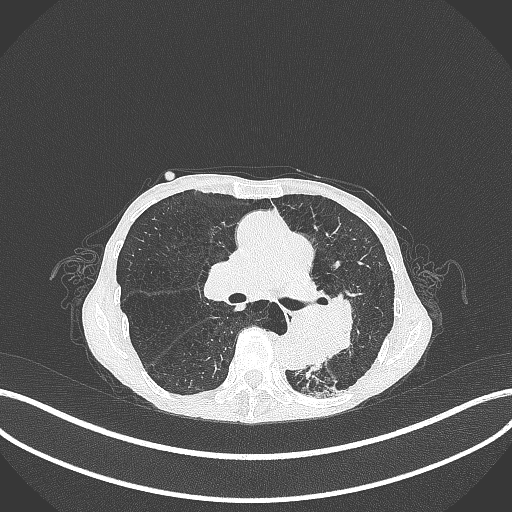
Chest CT, one axial slice; position 160 of 347 along the scan axis; 120 kVp; lung window (W 1500 / L -600 HU); 512 × 512 image matrix, field of view 400 × 400 mm. Patient: female, 70 years. Case-level facts recorded for this patient, not image findings: clinical TNM (as recorded): T3 N0 M0; histopathological grade: G3.
Annotated regions visible in this slice (rectangle marked by the reading radiologist):
- lung tumour (recorded histology: small cell carcinoma): bounding box [x1, y1, x2, y2] px = [281, 297, 356, 361]